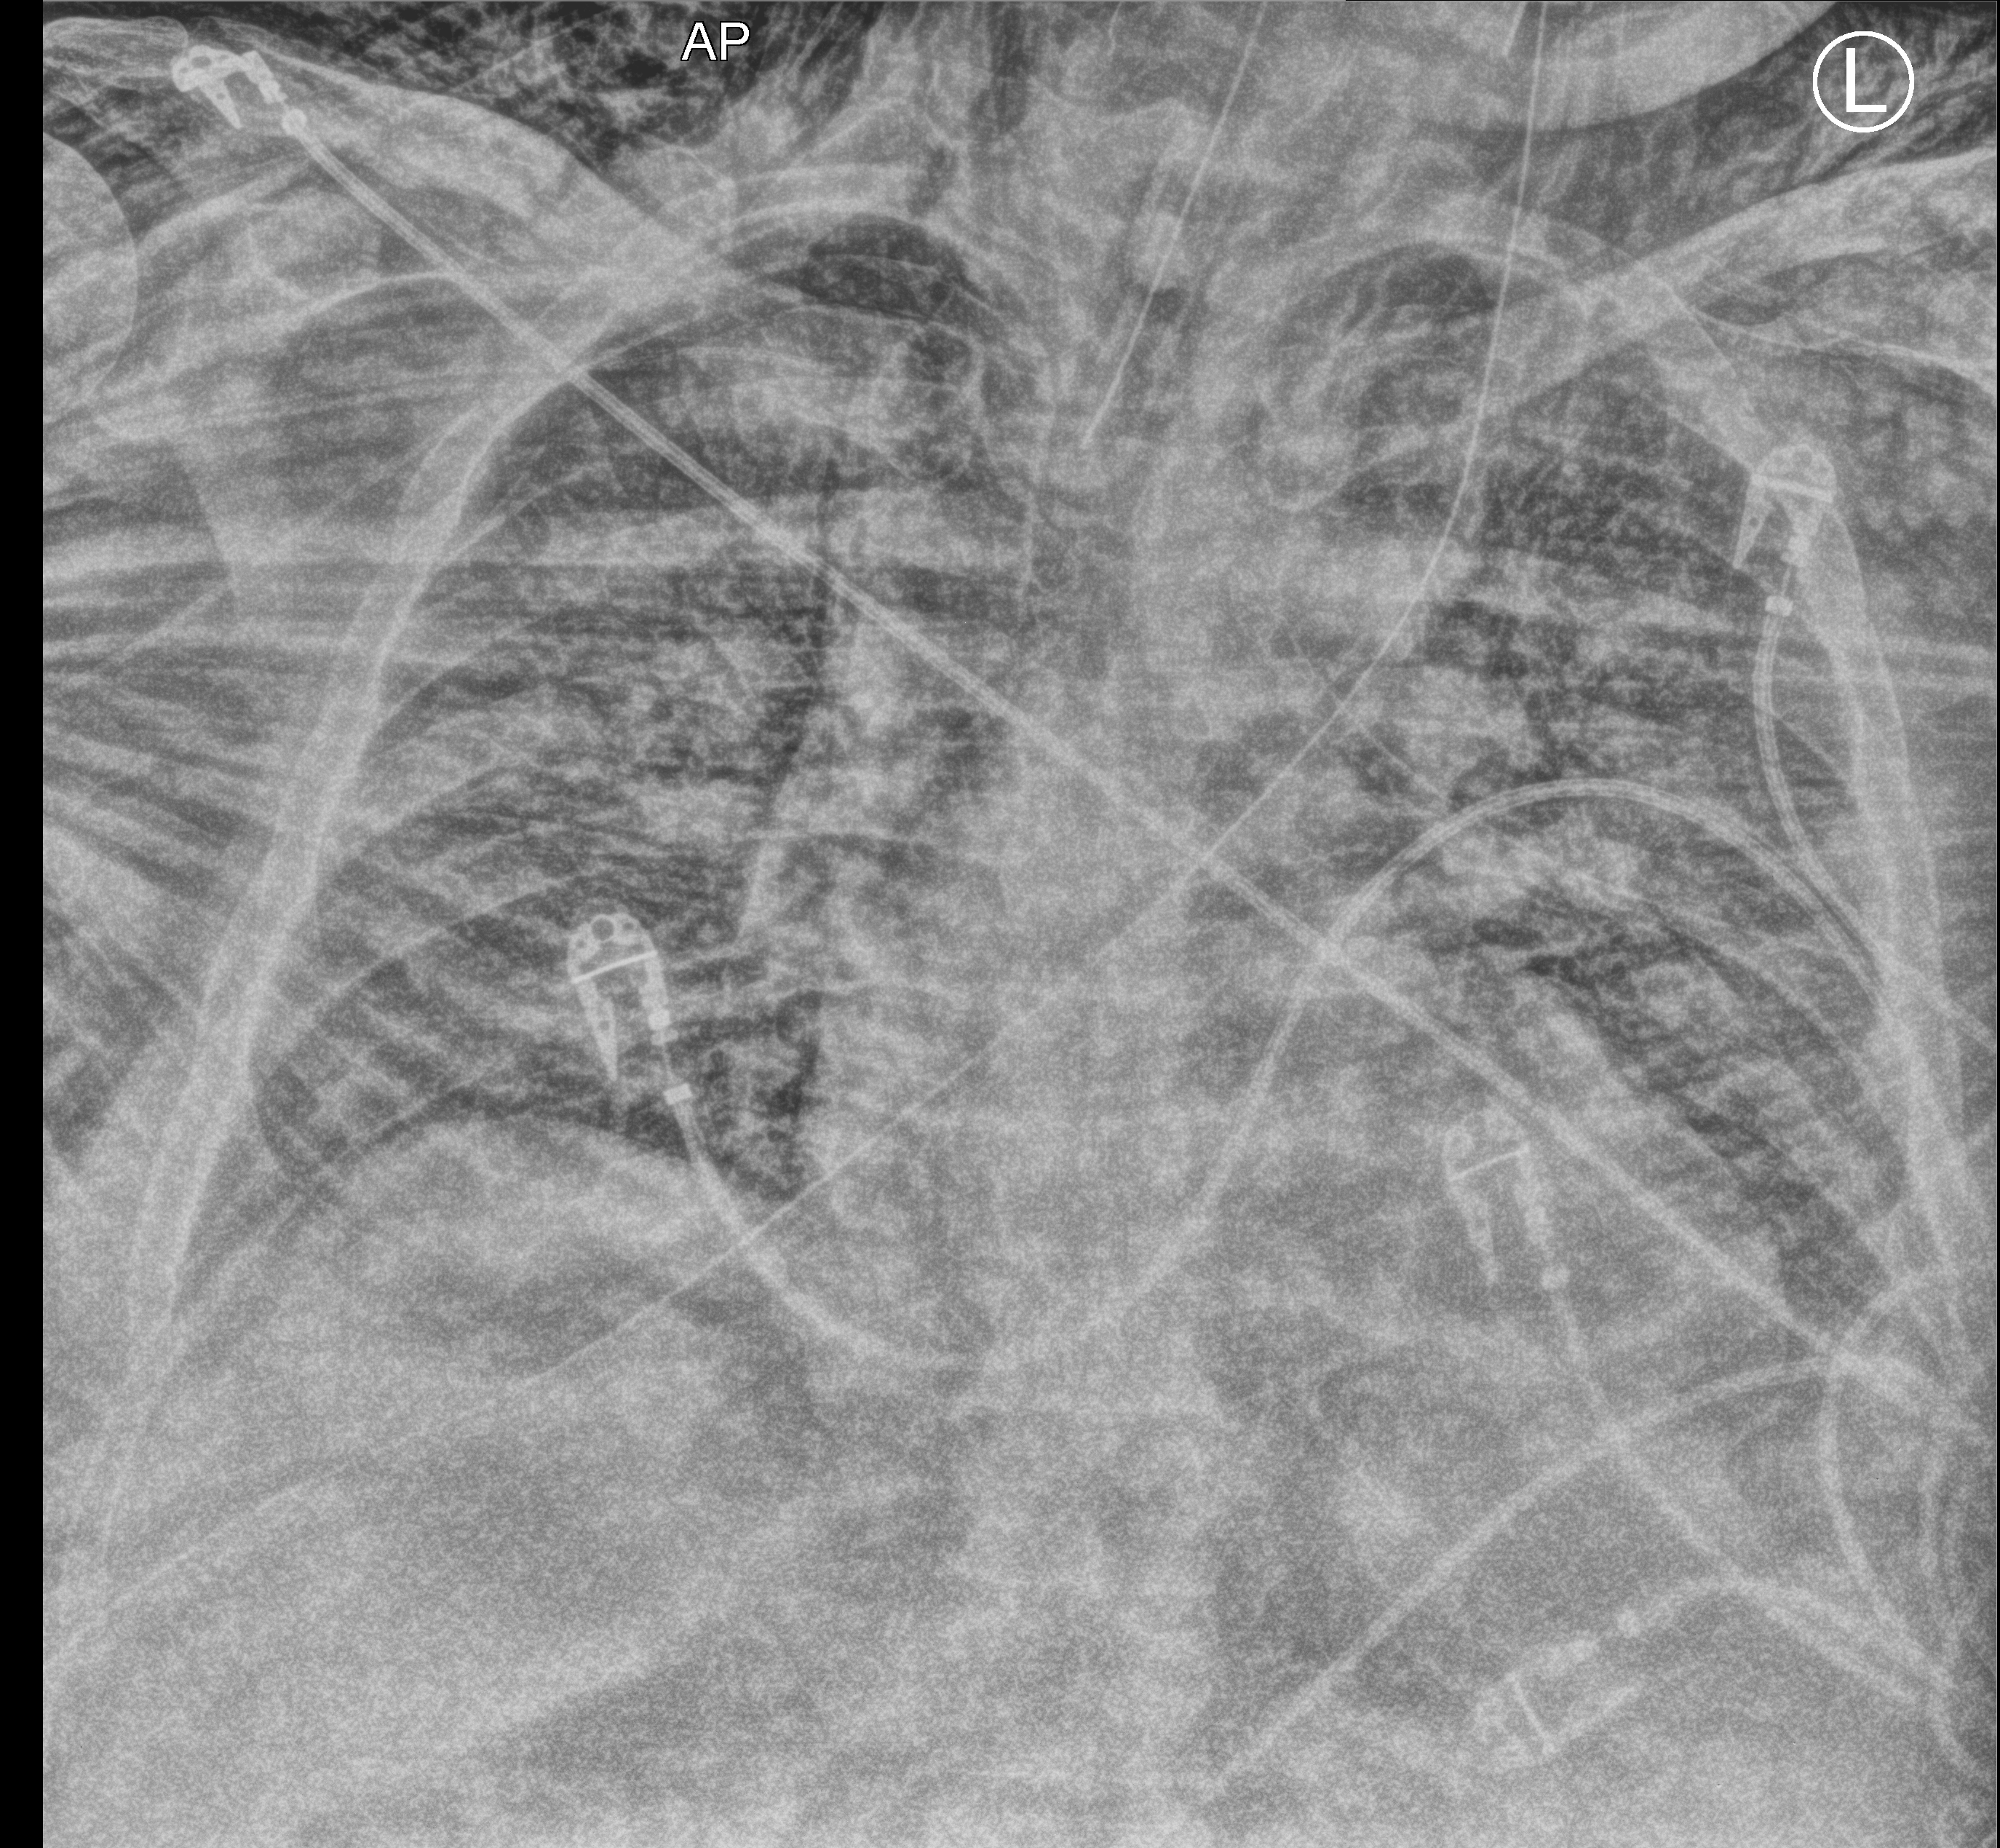
Portable chest radiograph; anteroposterior (AP) projection. Adult patient hospitalised with COVID-19, age 18–59 years.
Hospital-stay facts (about this admission, not read from this image; timing relative to this image not recorded): admitted to intensive care during this hospital stay: yes; other chronic lung disease (admission record): no; mechanically ventilated during this hospital stay: yes.